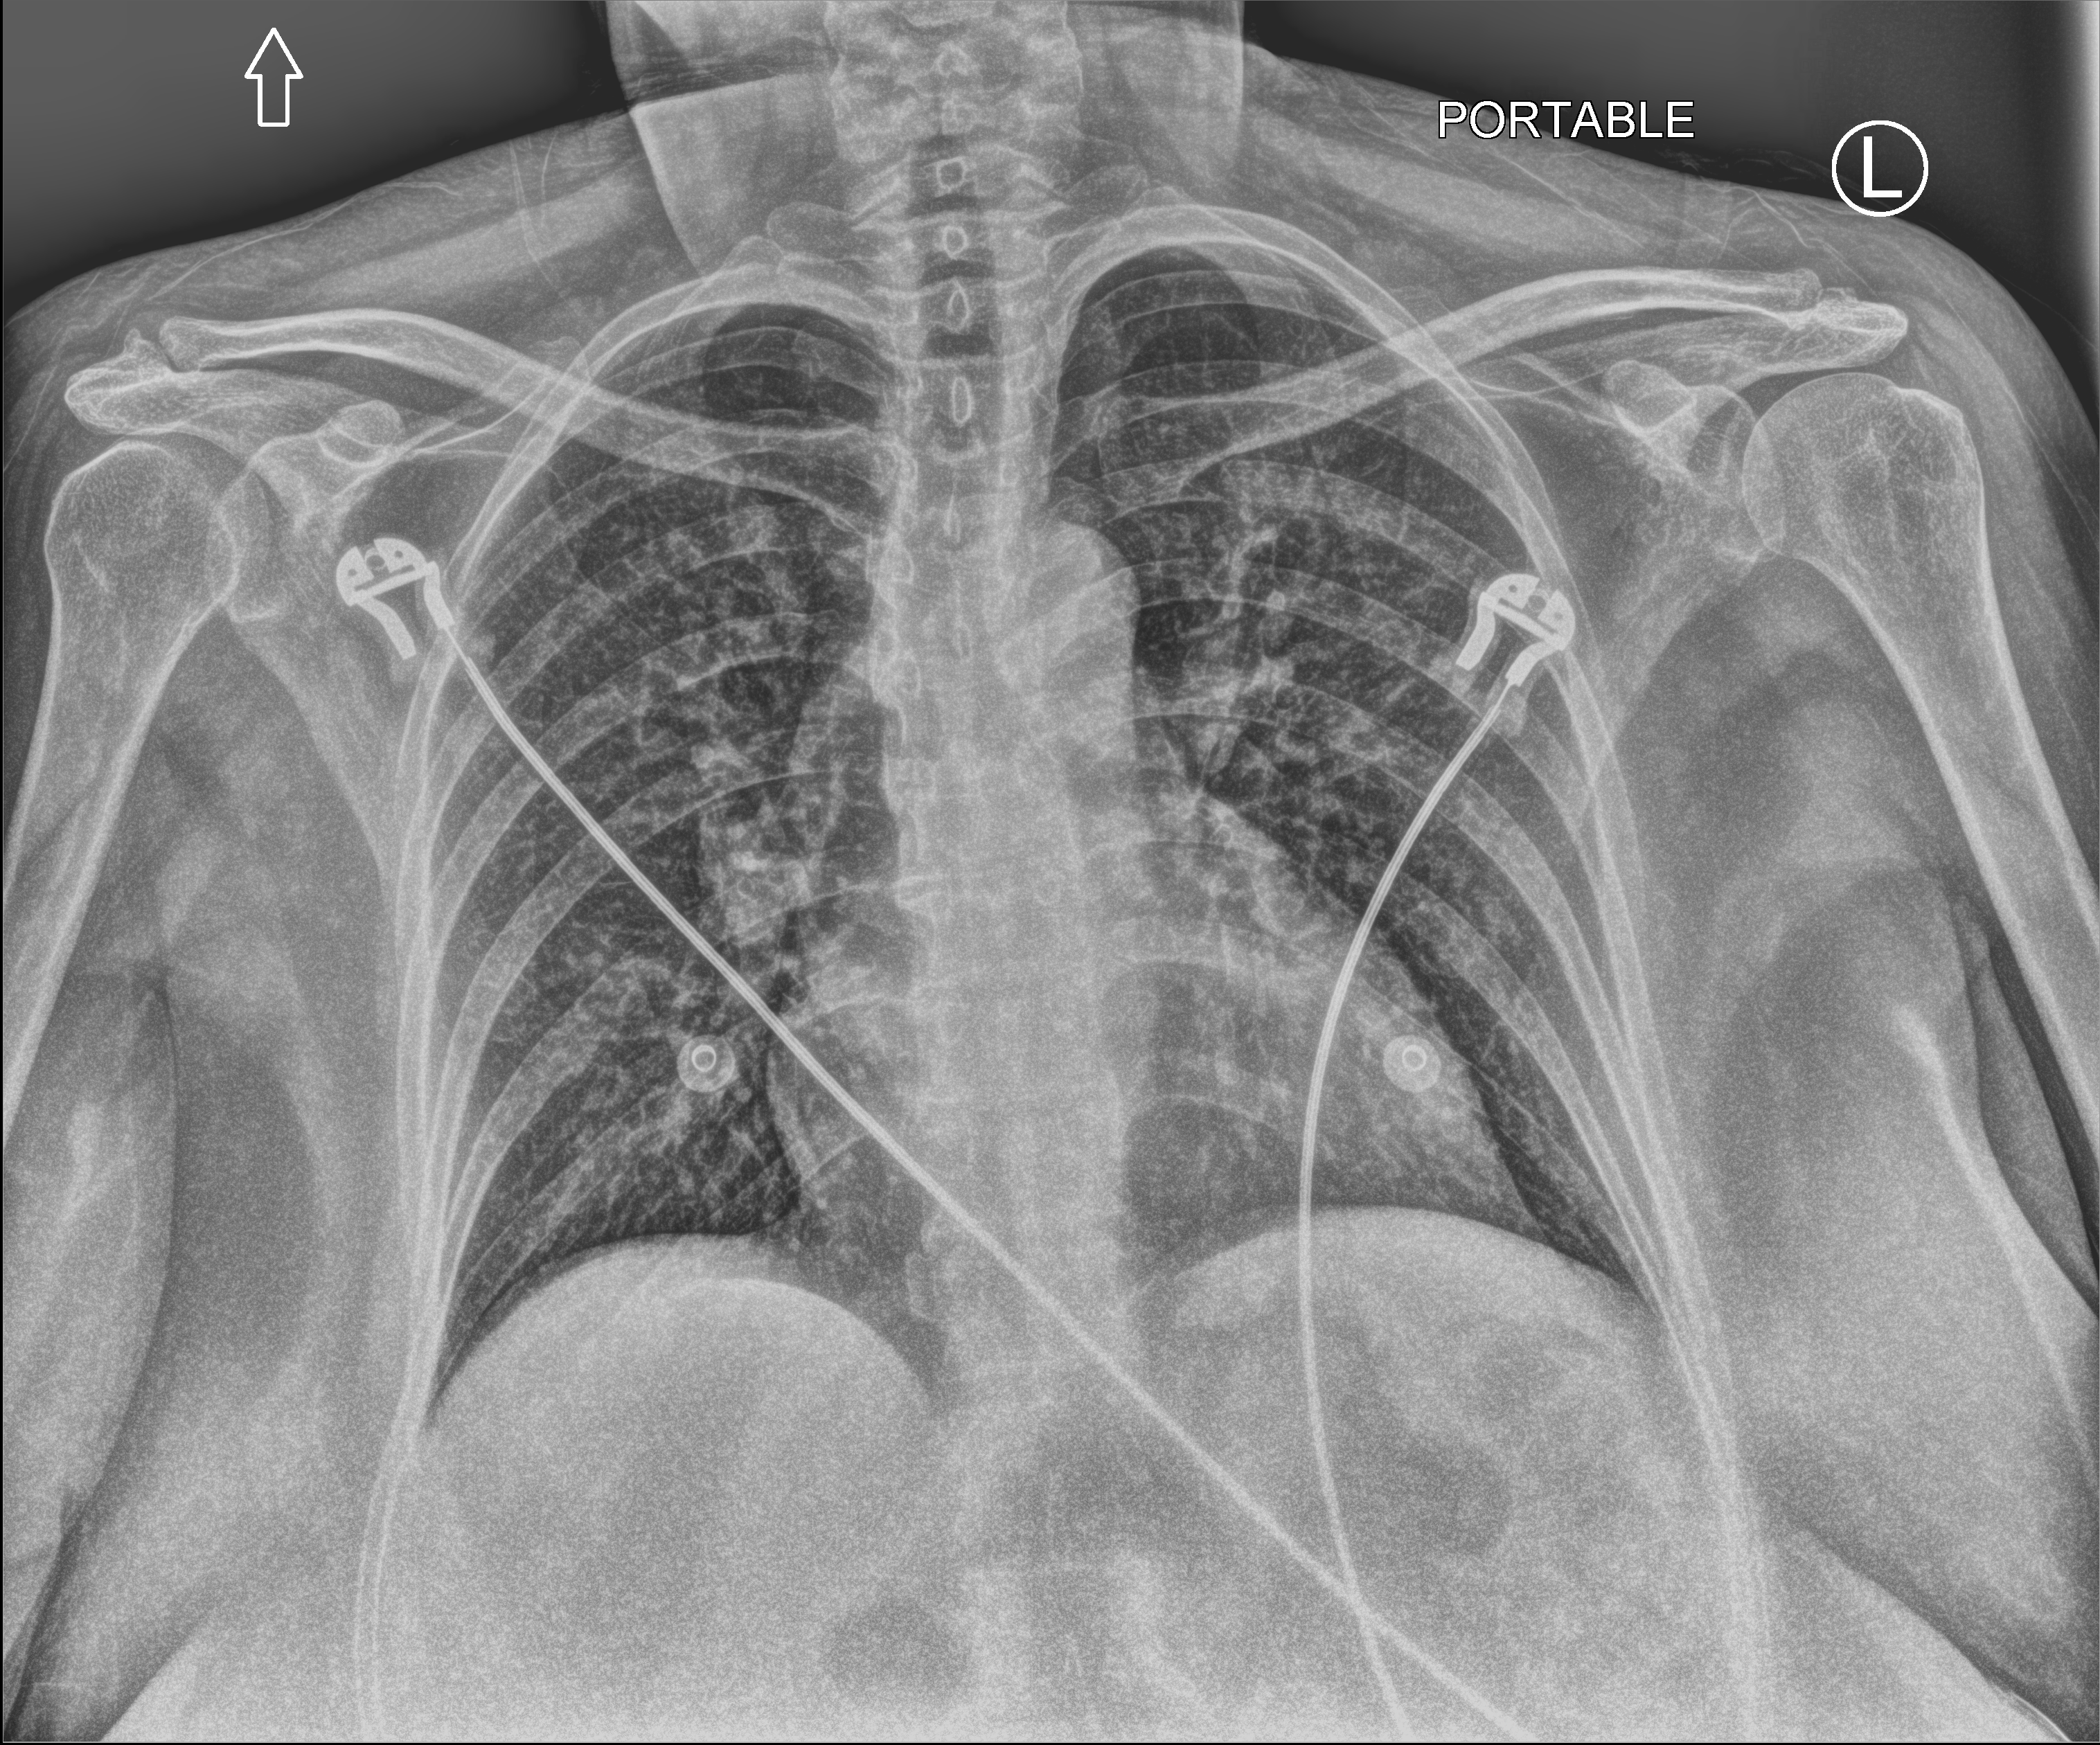
Chest X-ray (portable); anteroposterior (AP) projection. Female patient hospitalised with COVID-19, age 18–59 years.
Hospital-stay facts (about this admission, not read from this image; timing relative to this image not recorded):
- mechanically ventilated during this hospital stay: no